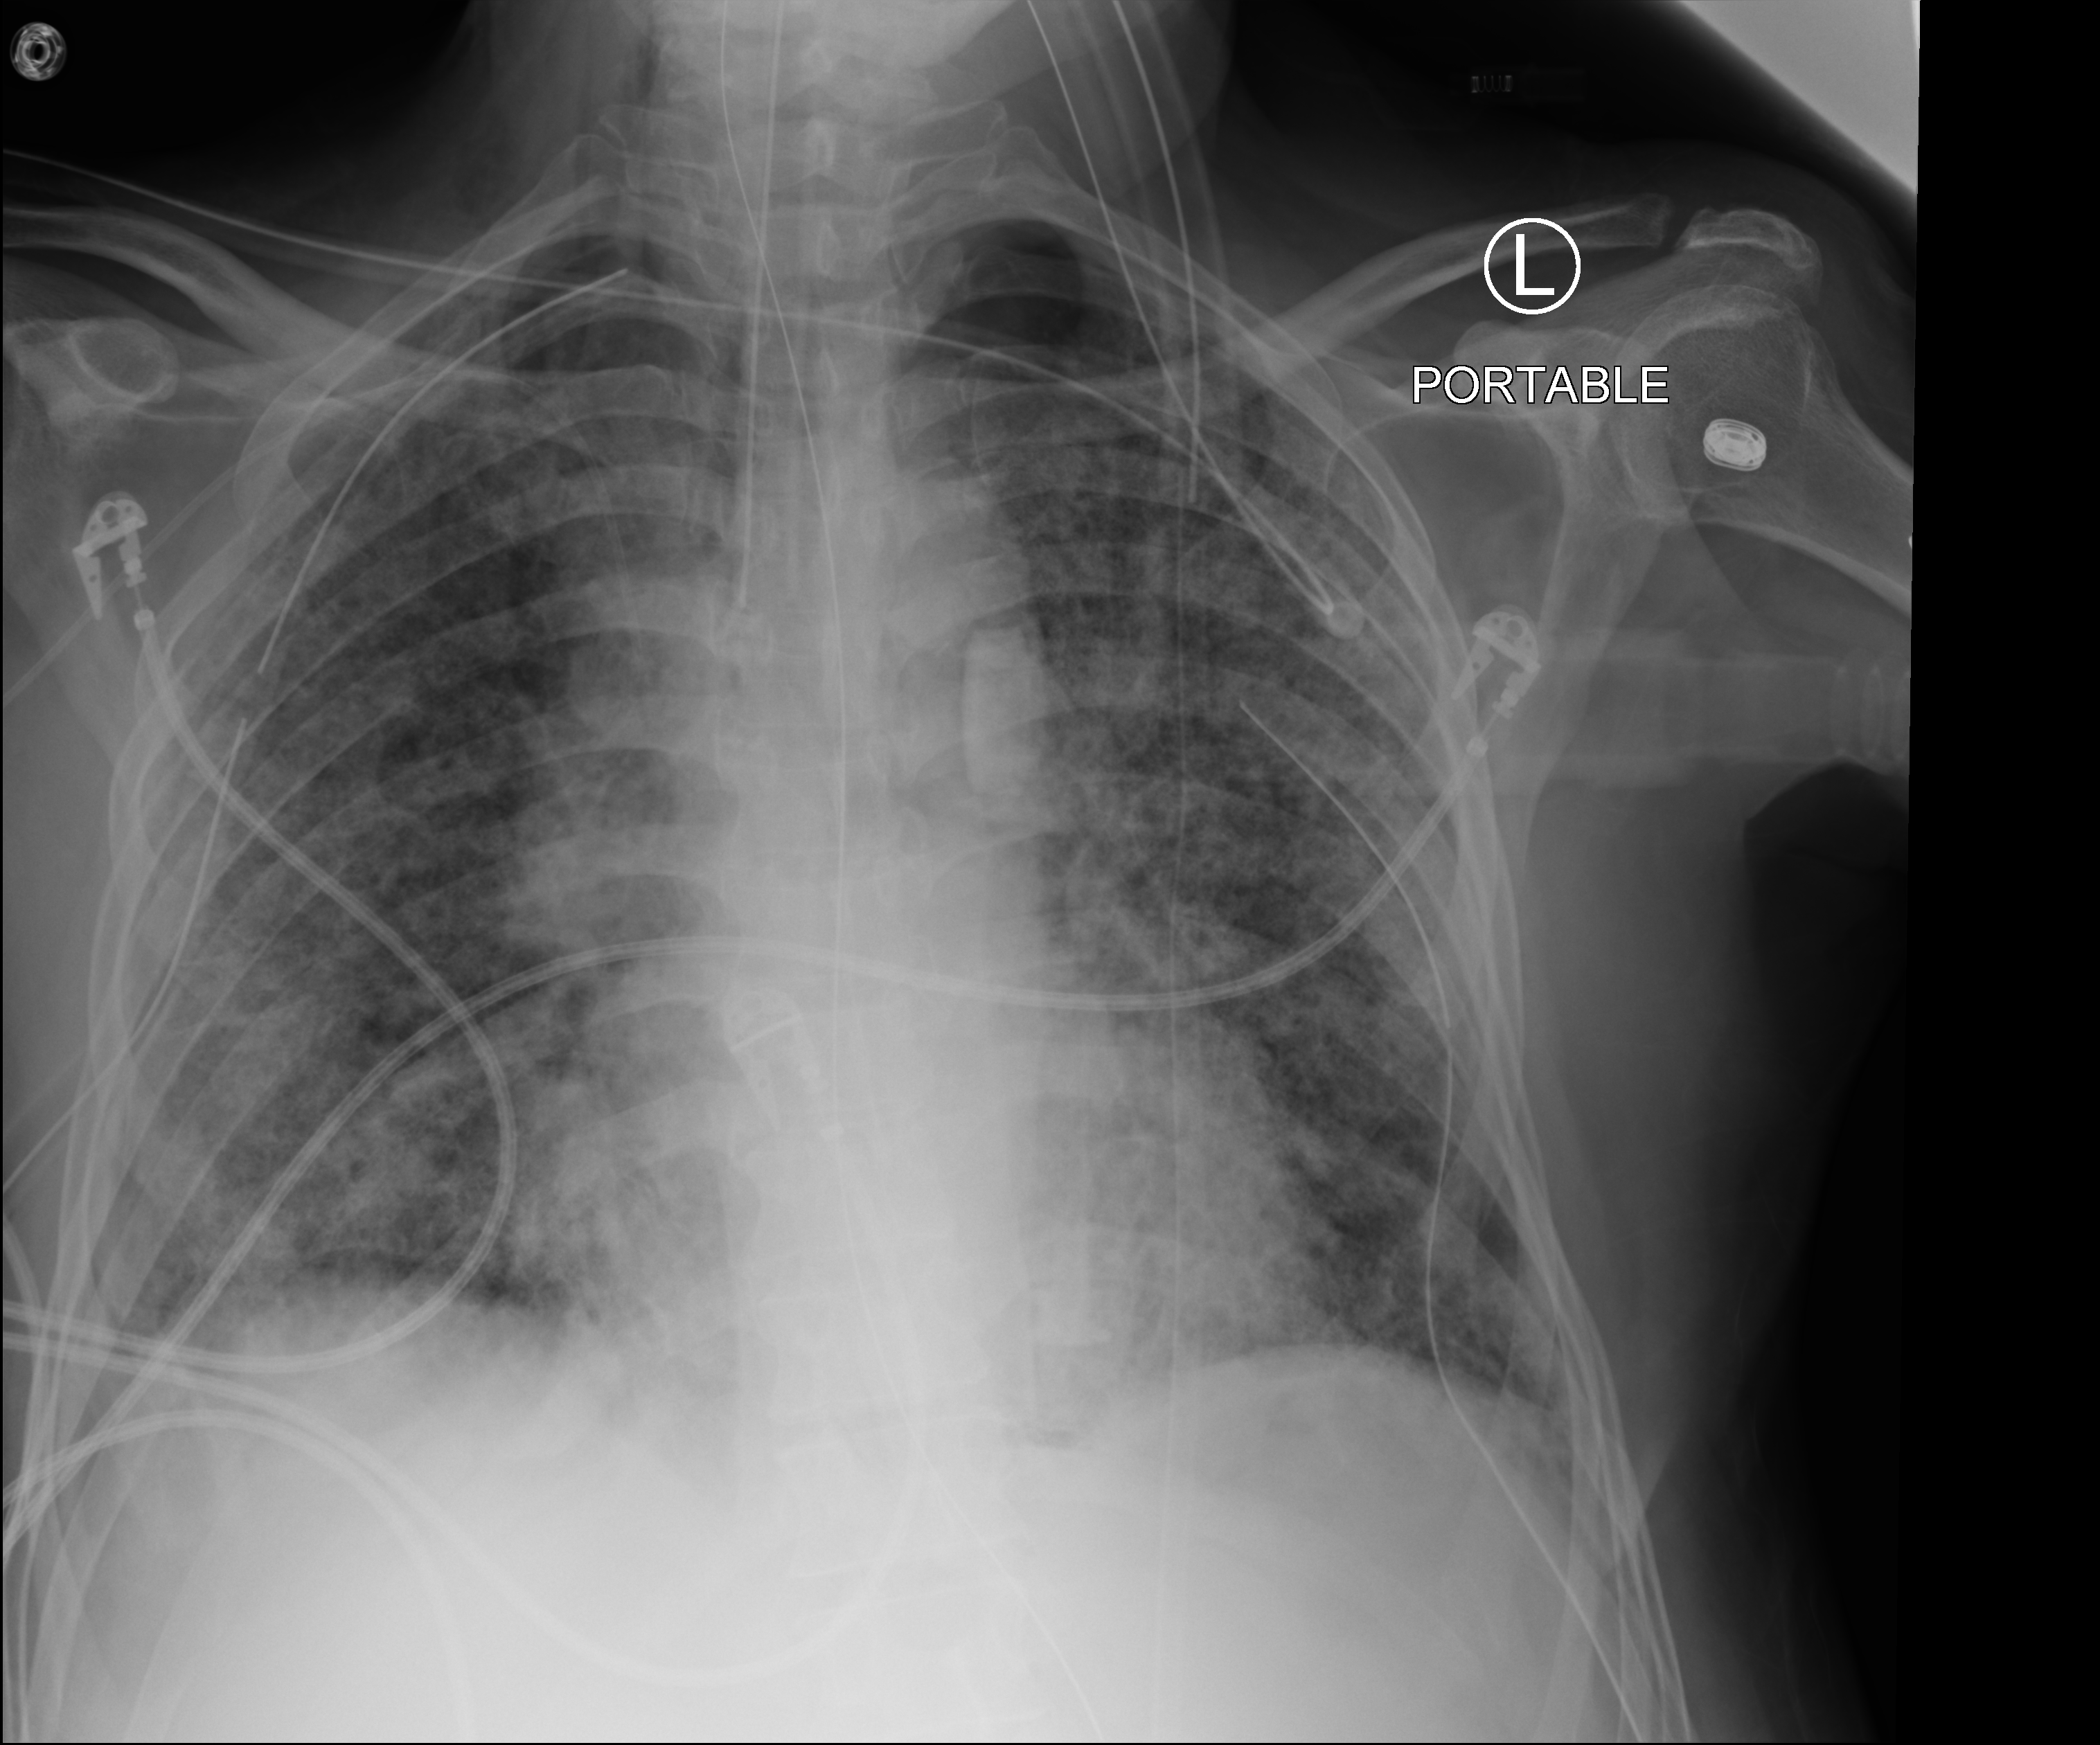
Bedside chest radiograph (computed radiography); anteroposterior (AP) projection. Patient hospitalised with COVID-19; male, aged 60–74 years.
From the hospital-stay record, not from the radiograph (when in the stay this image was taken is not recorded): diabetes (admission record): no; admitted to intensive care during this hospital stay: yes; mechanically ventilated during this hospital stay: yes.